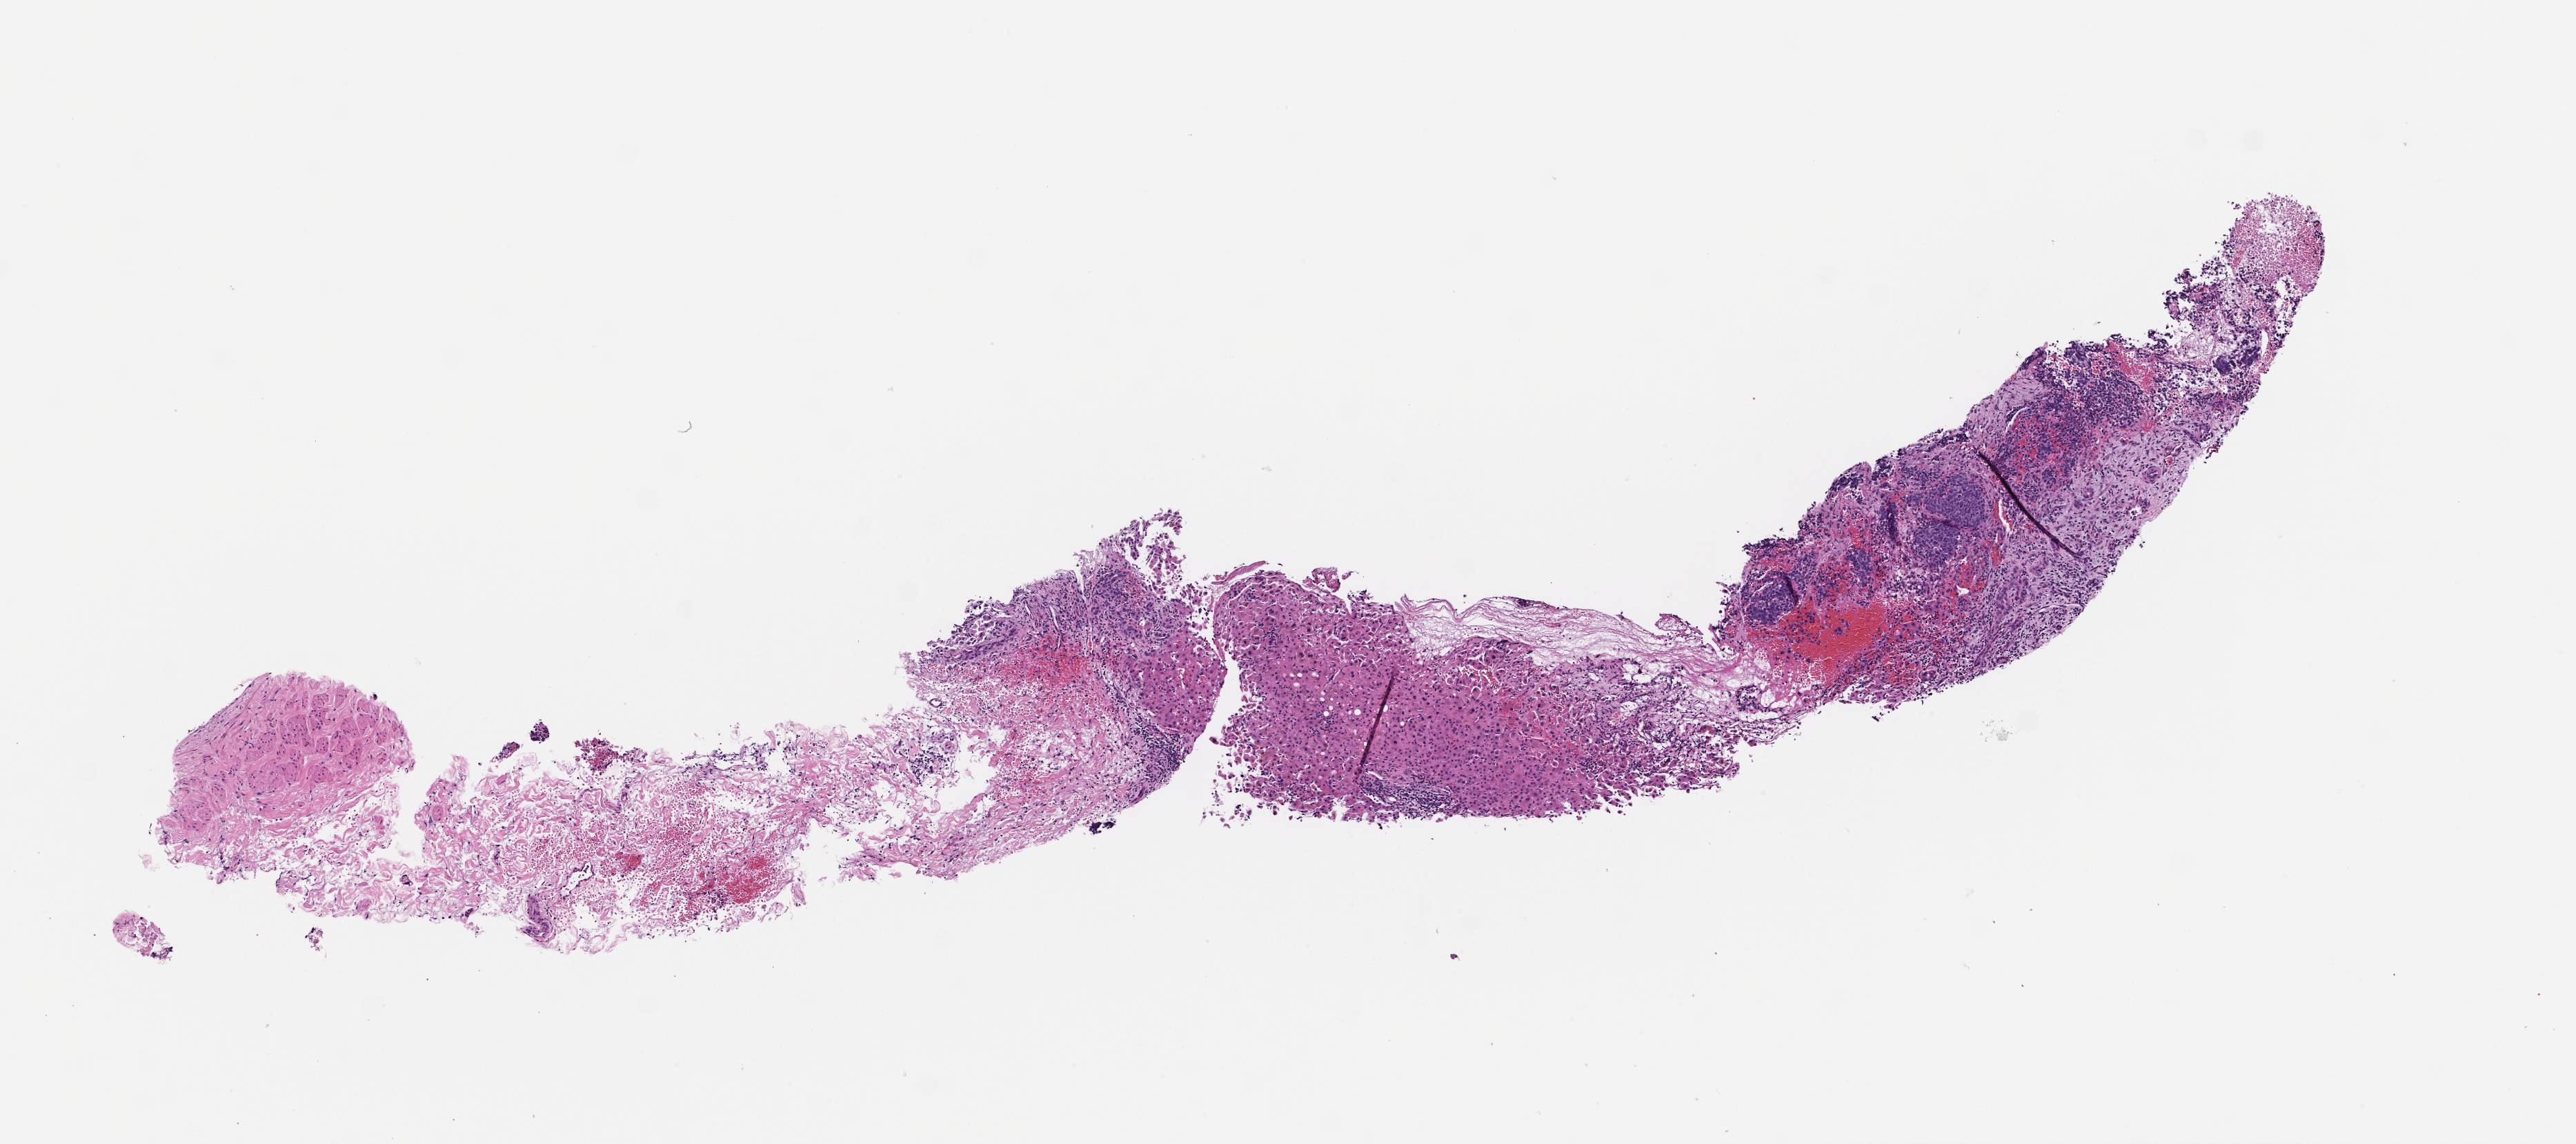
Digitized haematoxylin and eosin-stained section — a low-resolution overview of the entire scanned area, about 7.5 x 3.3 mm. Formalin-fixed paraffin-embedded section. Female patient.
This section: metastasis (sampled organ not recorded). Primary diagnosis of the patient: Non-Small Cell Lung Carcinoma.